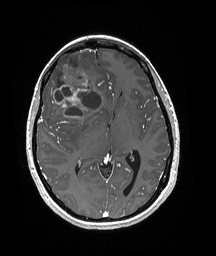
Brain MRI from a brain-tumour surgery series, one axial slice. T1-weighted post-contrast. 1 mm slice thickness. 216 × 256 image matrix, field of view 211 × 250 mm. Case-level facts recorded for this patient, not image findings: histopathology: Oligodendroglioma; WHO grade: 3.
Annotated regions visible in this slice (expert manual segmentation):
- tumour: bounding box (x1, y1, x2, y2) in pixels: (47, 53, 101, 118)